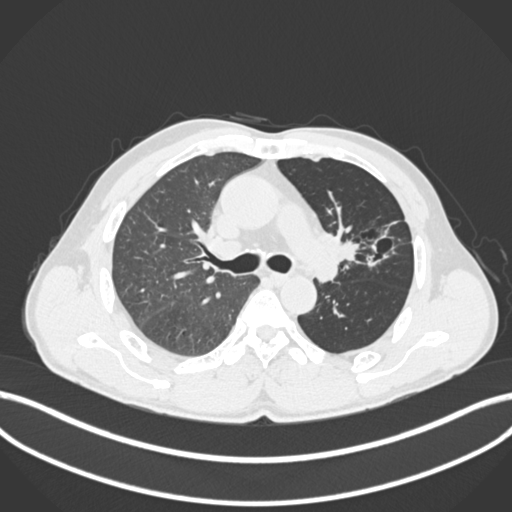
Chest CT, one axial slice; reconstruction kernel B30f; lung window (W 1500 / L -600 HU); 1 mm slice thickness; 512 × 512 image matrix, field of view 400 × 400 mm. Patient: male, 57 years. From the clinical record (not read from this slice): clinical TNM (as recorded): T2b N0 M0.
Outlined on this slice (bounding box drawn by a radiologist):
- lung tumour (recorded histology: squamous cell carcinoma): bounding box (x1, y1, x2, y2) in pixels: (318, 225, 371, 263)